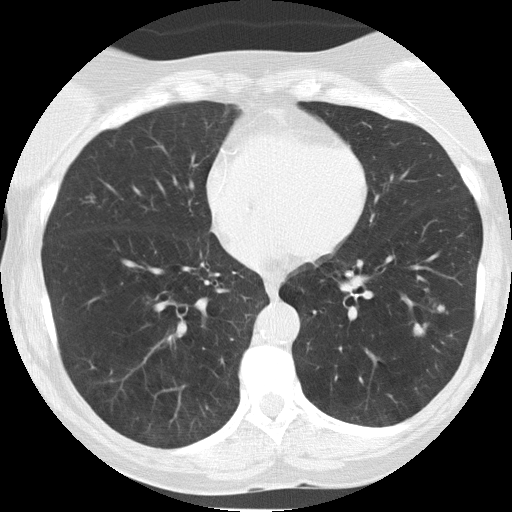
Axial slice from a low-dose chest CT screening exam. First (baseline) screen. Lung window (W 1500 / L -600 HU). 512 × 512 image matrix. Female participant, aged 58 years at enrolment.
Lesion marked by an expert reader, bounding box <408,298,458,344> (left, top, right, bottom; pixels). The screening reader recorded 3 non-calcified nodules or masses ≥4 mm on this exam (right lower lobe, lingula, left lower lobe); which of them this box marks is not recorded. Later outcome: lung cancer diagnosed 93 days after this screen — adenocarcinoma, NOS, left lower lobe, moderately differentiated (G2), stage IIIB (AJCC 6th edition), 14 mm at pathology.